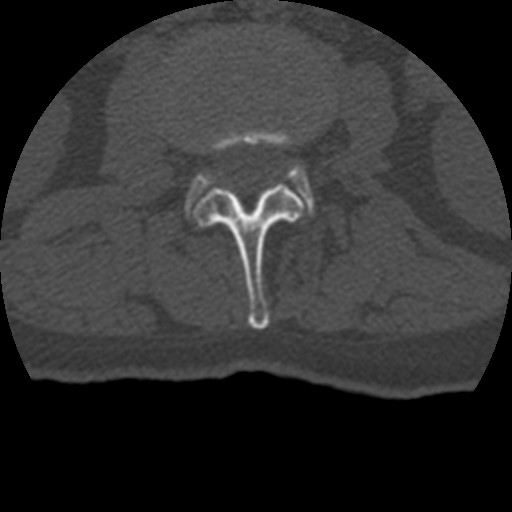
CT including the spine, one axial slice; slice 107 of 399 in the series (ordered by position); reconstruction kernel STANDARD; 120 kVp; bone window (W 1800 / L 400 HU); 1.25 mm slice thickness; 512 × 512 image matrix, field of view 160 × 160 mm. Patient age 69 years. Case-level facts recorded for this patient, not image findings: primary cancer: prostate.
Structures marked on this image (semi-automatically segmented with operator editing):
- L2 vertebra: box from (x=194, y=129) to (x=304, y=329) px
- L3 vertebra: (x=189, y=166)–(x=313, y=202)